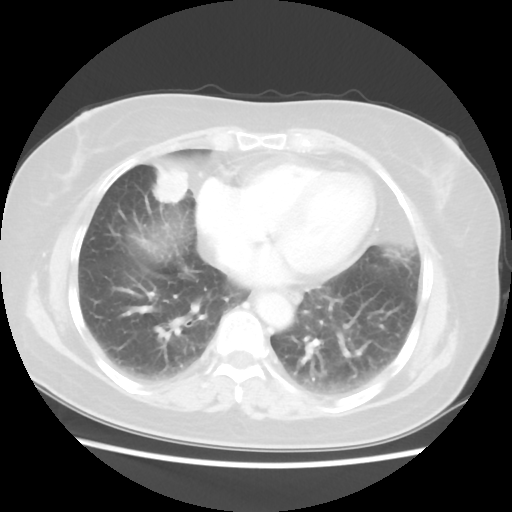
Chest CT, one axial slice; position 19 of 48 along the scan axis; reconstruction kernel STANDARD; lung window (W 1500 / L -600 HU); 5 mm slice thickness; 512 × 512 image matrix, field of view 343 × 343 mm. Female patient, age 61 years. Case-level facts recorded for this patient, not image findings: clinical TNM (as recorded): T1c N0 M0.
Structures marked on this image (bounding box drawn by a radiologist):
- lung tumour (recorded histology: adenocarcinoma): bounding box [x1, y1, x2, y2] px = [148, 159, 191, 206]